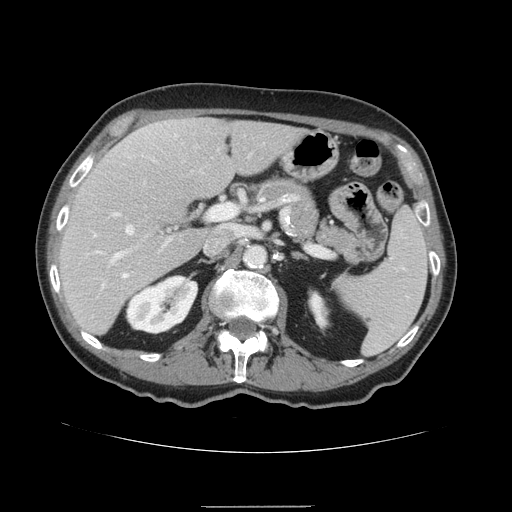
Contrast-enhanced abdominal CT, one axial slice; intravenous contrast given; soft-tissue window (W 400 / L 40 HU); 2.5 mm slice thickness; 512 × 512 image matrix, field of view 386 × 386 mm. Male patient, age 74 years. From the clinical record (not read from this slice): diagnosis: colorectal cancer liver metastases, imaged before liver resection.
Annotated regions visible in this slice (manually delineated by an expert):
- hepatic veins: bounding box [x1, y1, x2, y2] px = [124, 225, 134, 277]
- liver: [59, 118, 308, 335]
- planned liver remnant (the part of the liver to remain after resection): [59, 120, 308, 335]
- portal vein (with intrahepatic branches): [86, 205, 235, 266]